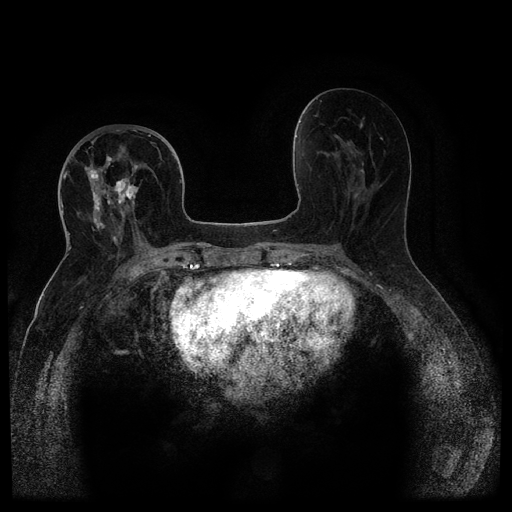
Breast MRI (dynamic contrast-enhanced, multi-phase), one axial slice; dynamic contrast-enhanced series, time point 2 of 5 at this slice position (early post-contrast); 1.5 T; TE 2.6 ms, TR 5.4 ms; 512 × 512 image matrix. Patient: female, 68 years.
Structures marked on this image (semi-automatically segmented with operator editing):
- breast lesion (labelled 'tumour' in the annotation; benign lesions carry a separate 'benign' label): box from (x=112, y=175) to (x=143, y=210) px
- breast lesion (labelled 'tumour' in the annotation; benign lesions carry a separate 'benign' label): (x=88, y=164)–(x=110, y=233)